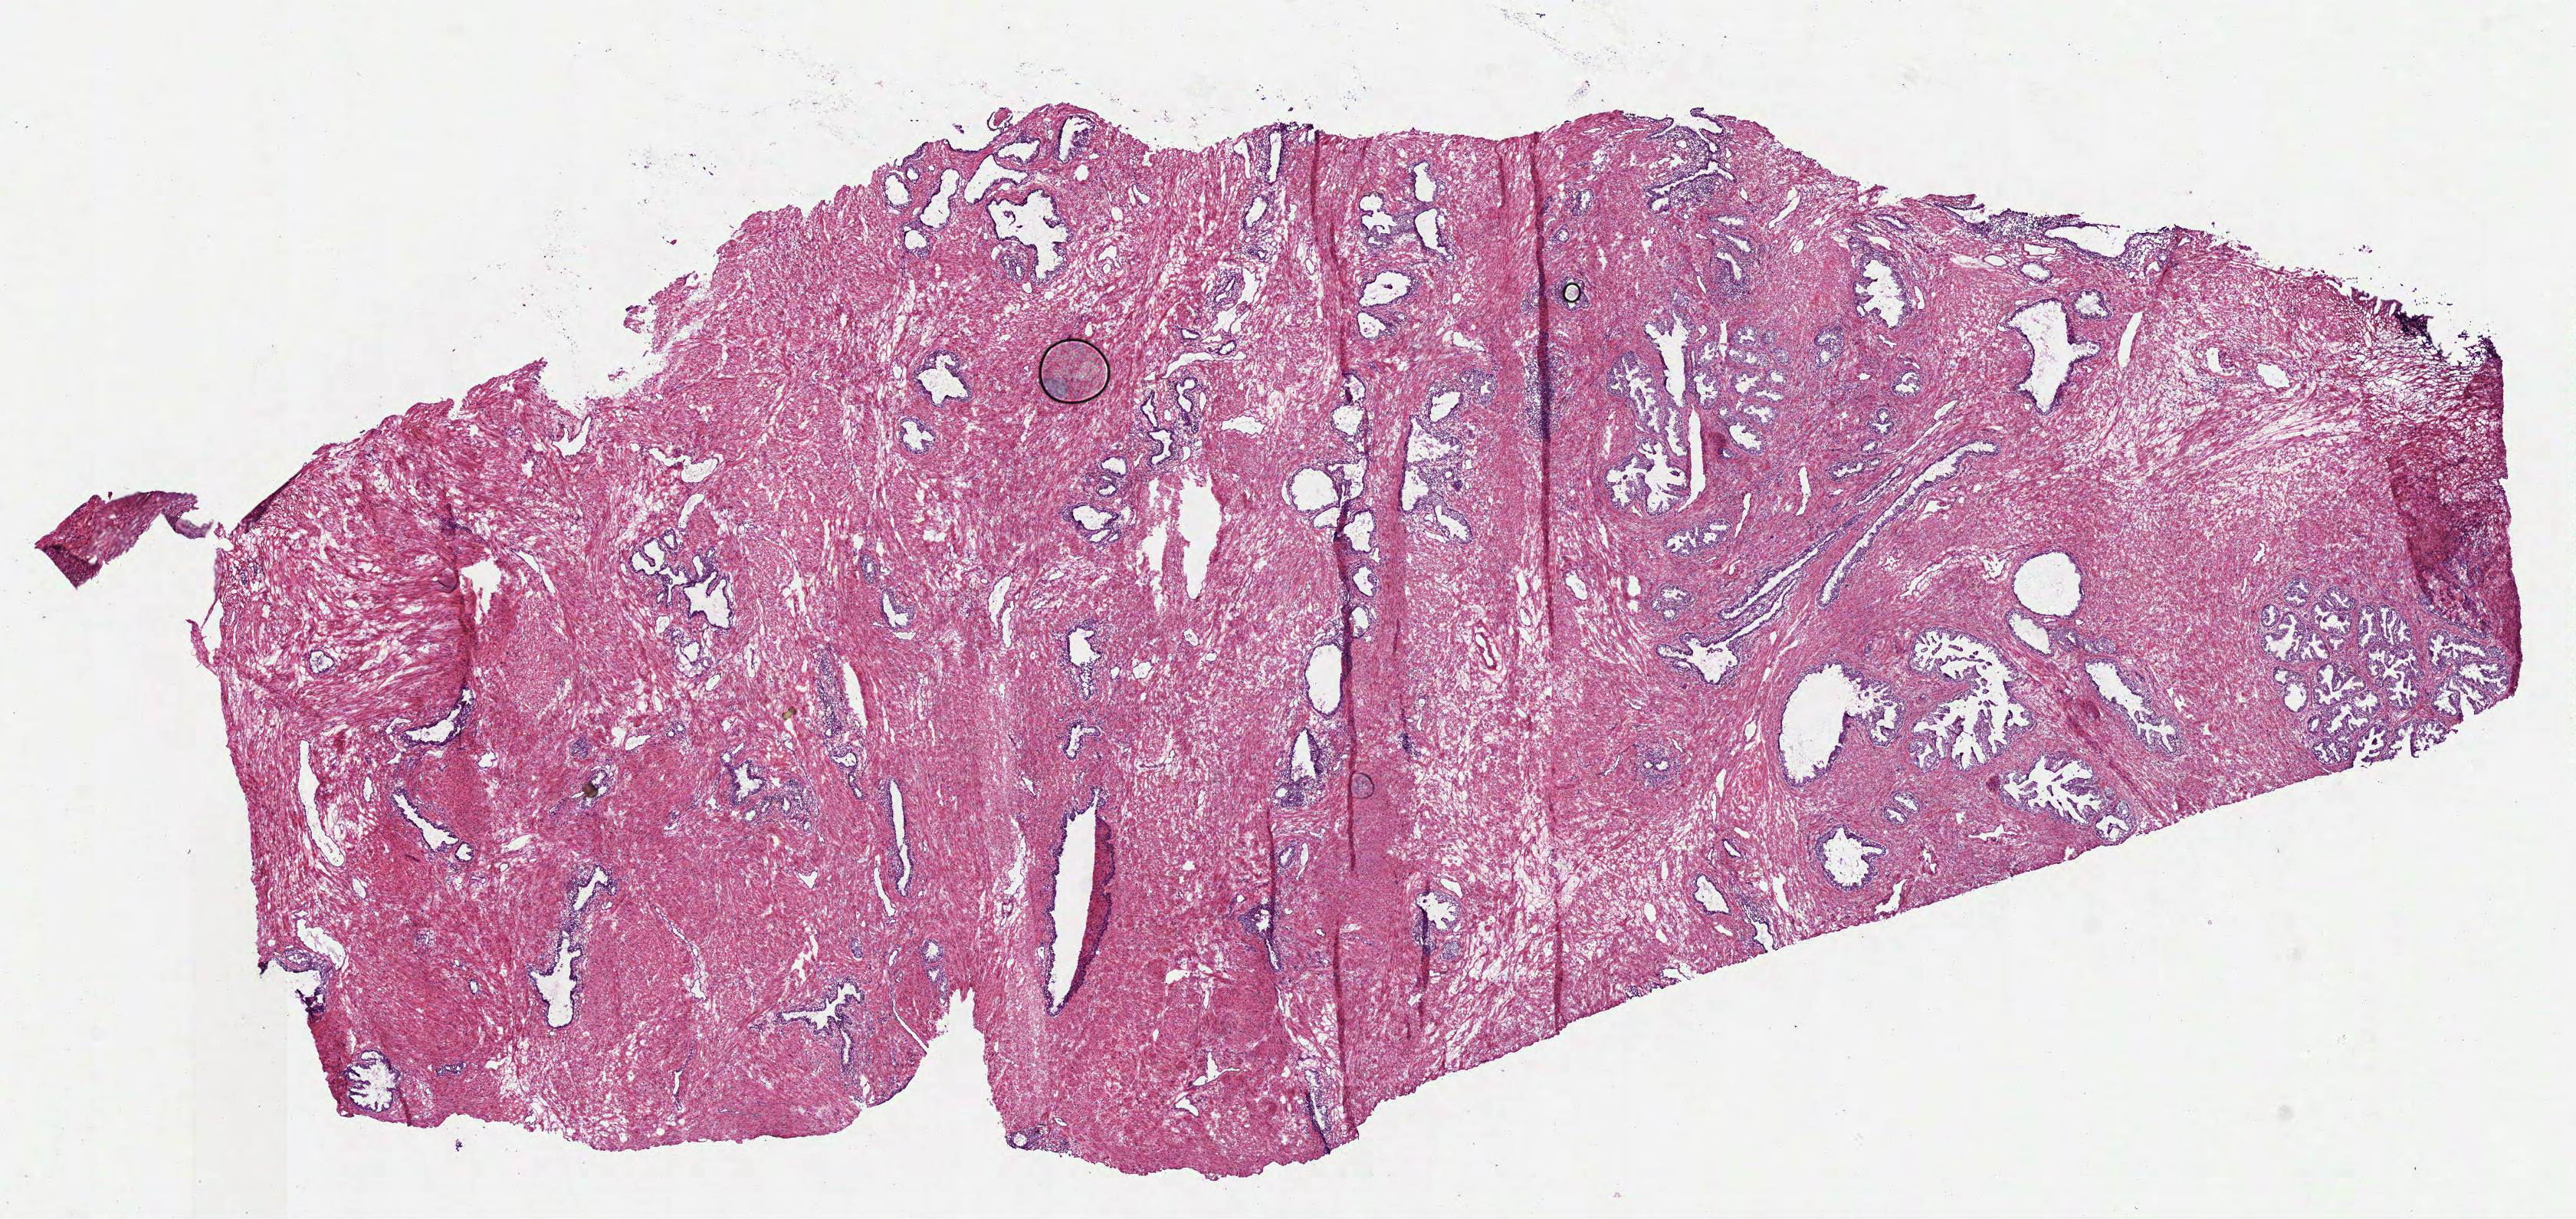
H&E whole-slide image, whole scanned area (about 13.6 x 6.4 mm, acquisition: 40x scan) shown as a low-resolution overview. Frozen section. Solid tissue normal (non-tumour tissue) sample from the prostate. Patient: male, age at initial diagnosis 69 years.
This section: solid tissue normal sample (biorepository sample class). Patient diagnosis: Acinar cell carcinoma (prostate gland).